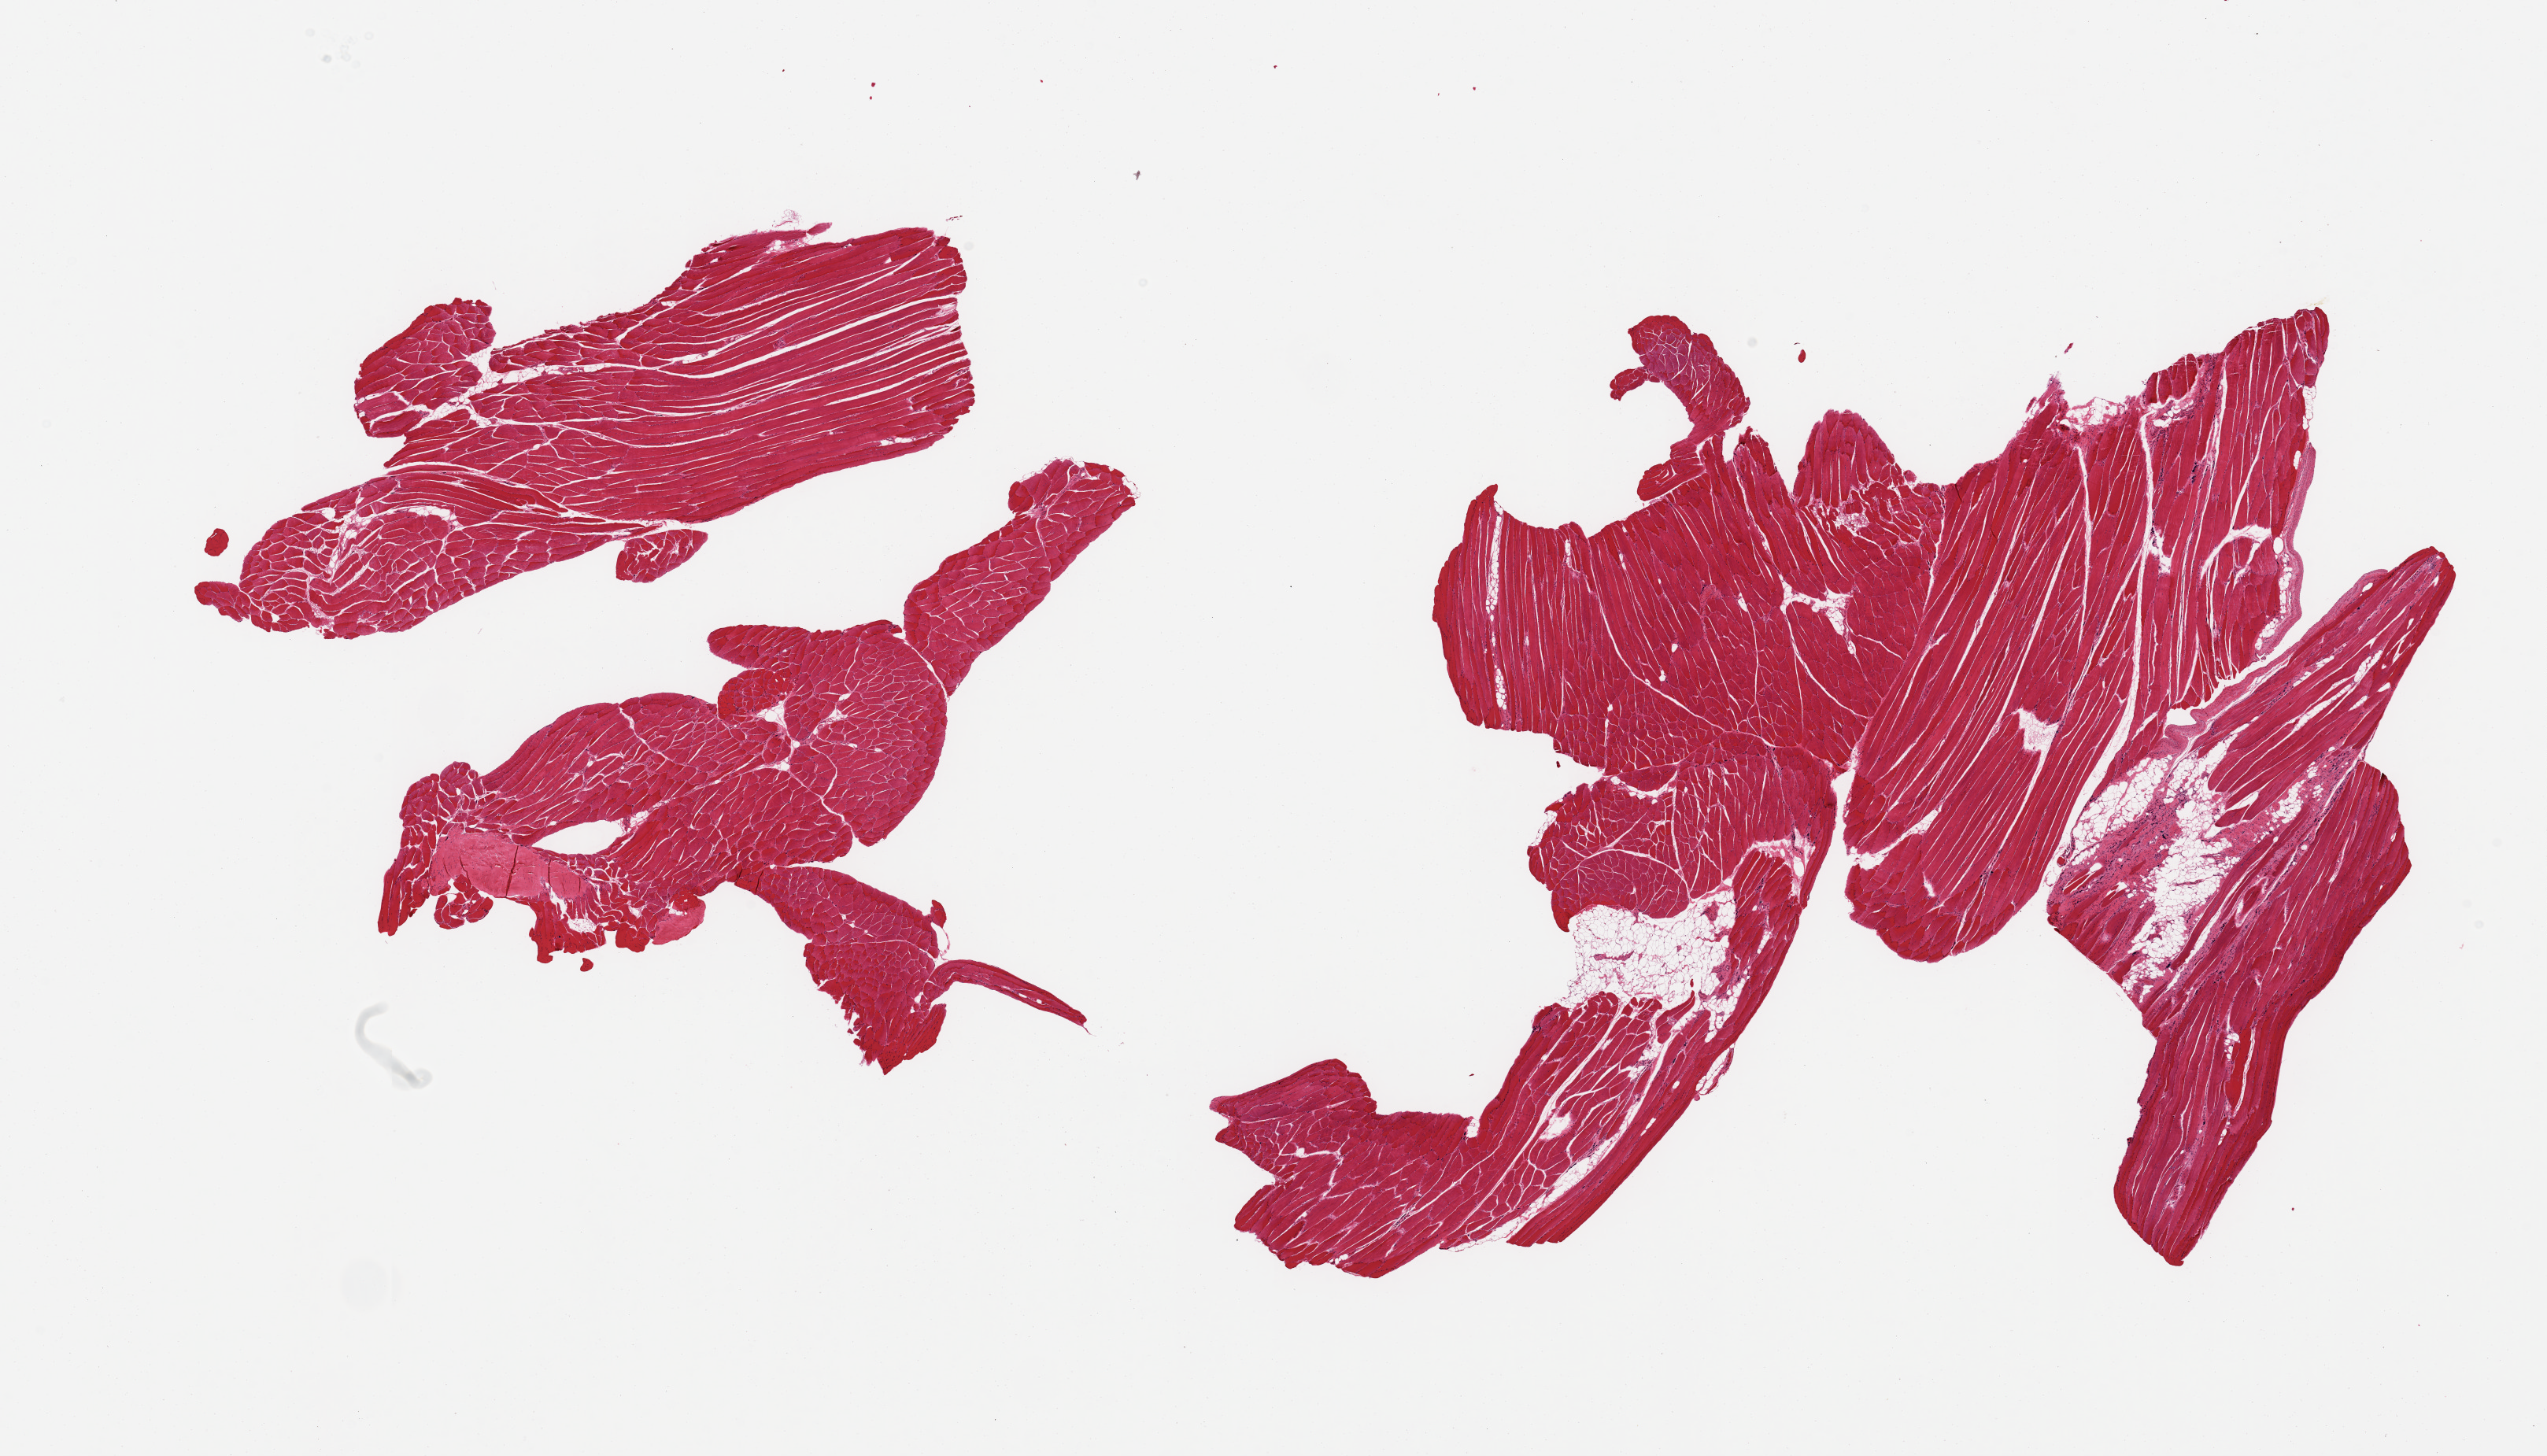
Digitized haematoxylin and eosin-stained section, brightfield, whole scanned area (about 25.6 x 14.6 mm) shown as a low-resolution overview; PAXgene-fixed paraffin-embedded (PFPE) section; section of skeletal muscle (target tissue); tissue donor sample. Donor sex: female.
• pathologist's review note for this sample: 2 pieces, ~5-10% interstitial fat; focal tendon insertion; focie of scarring